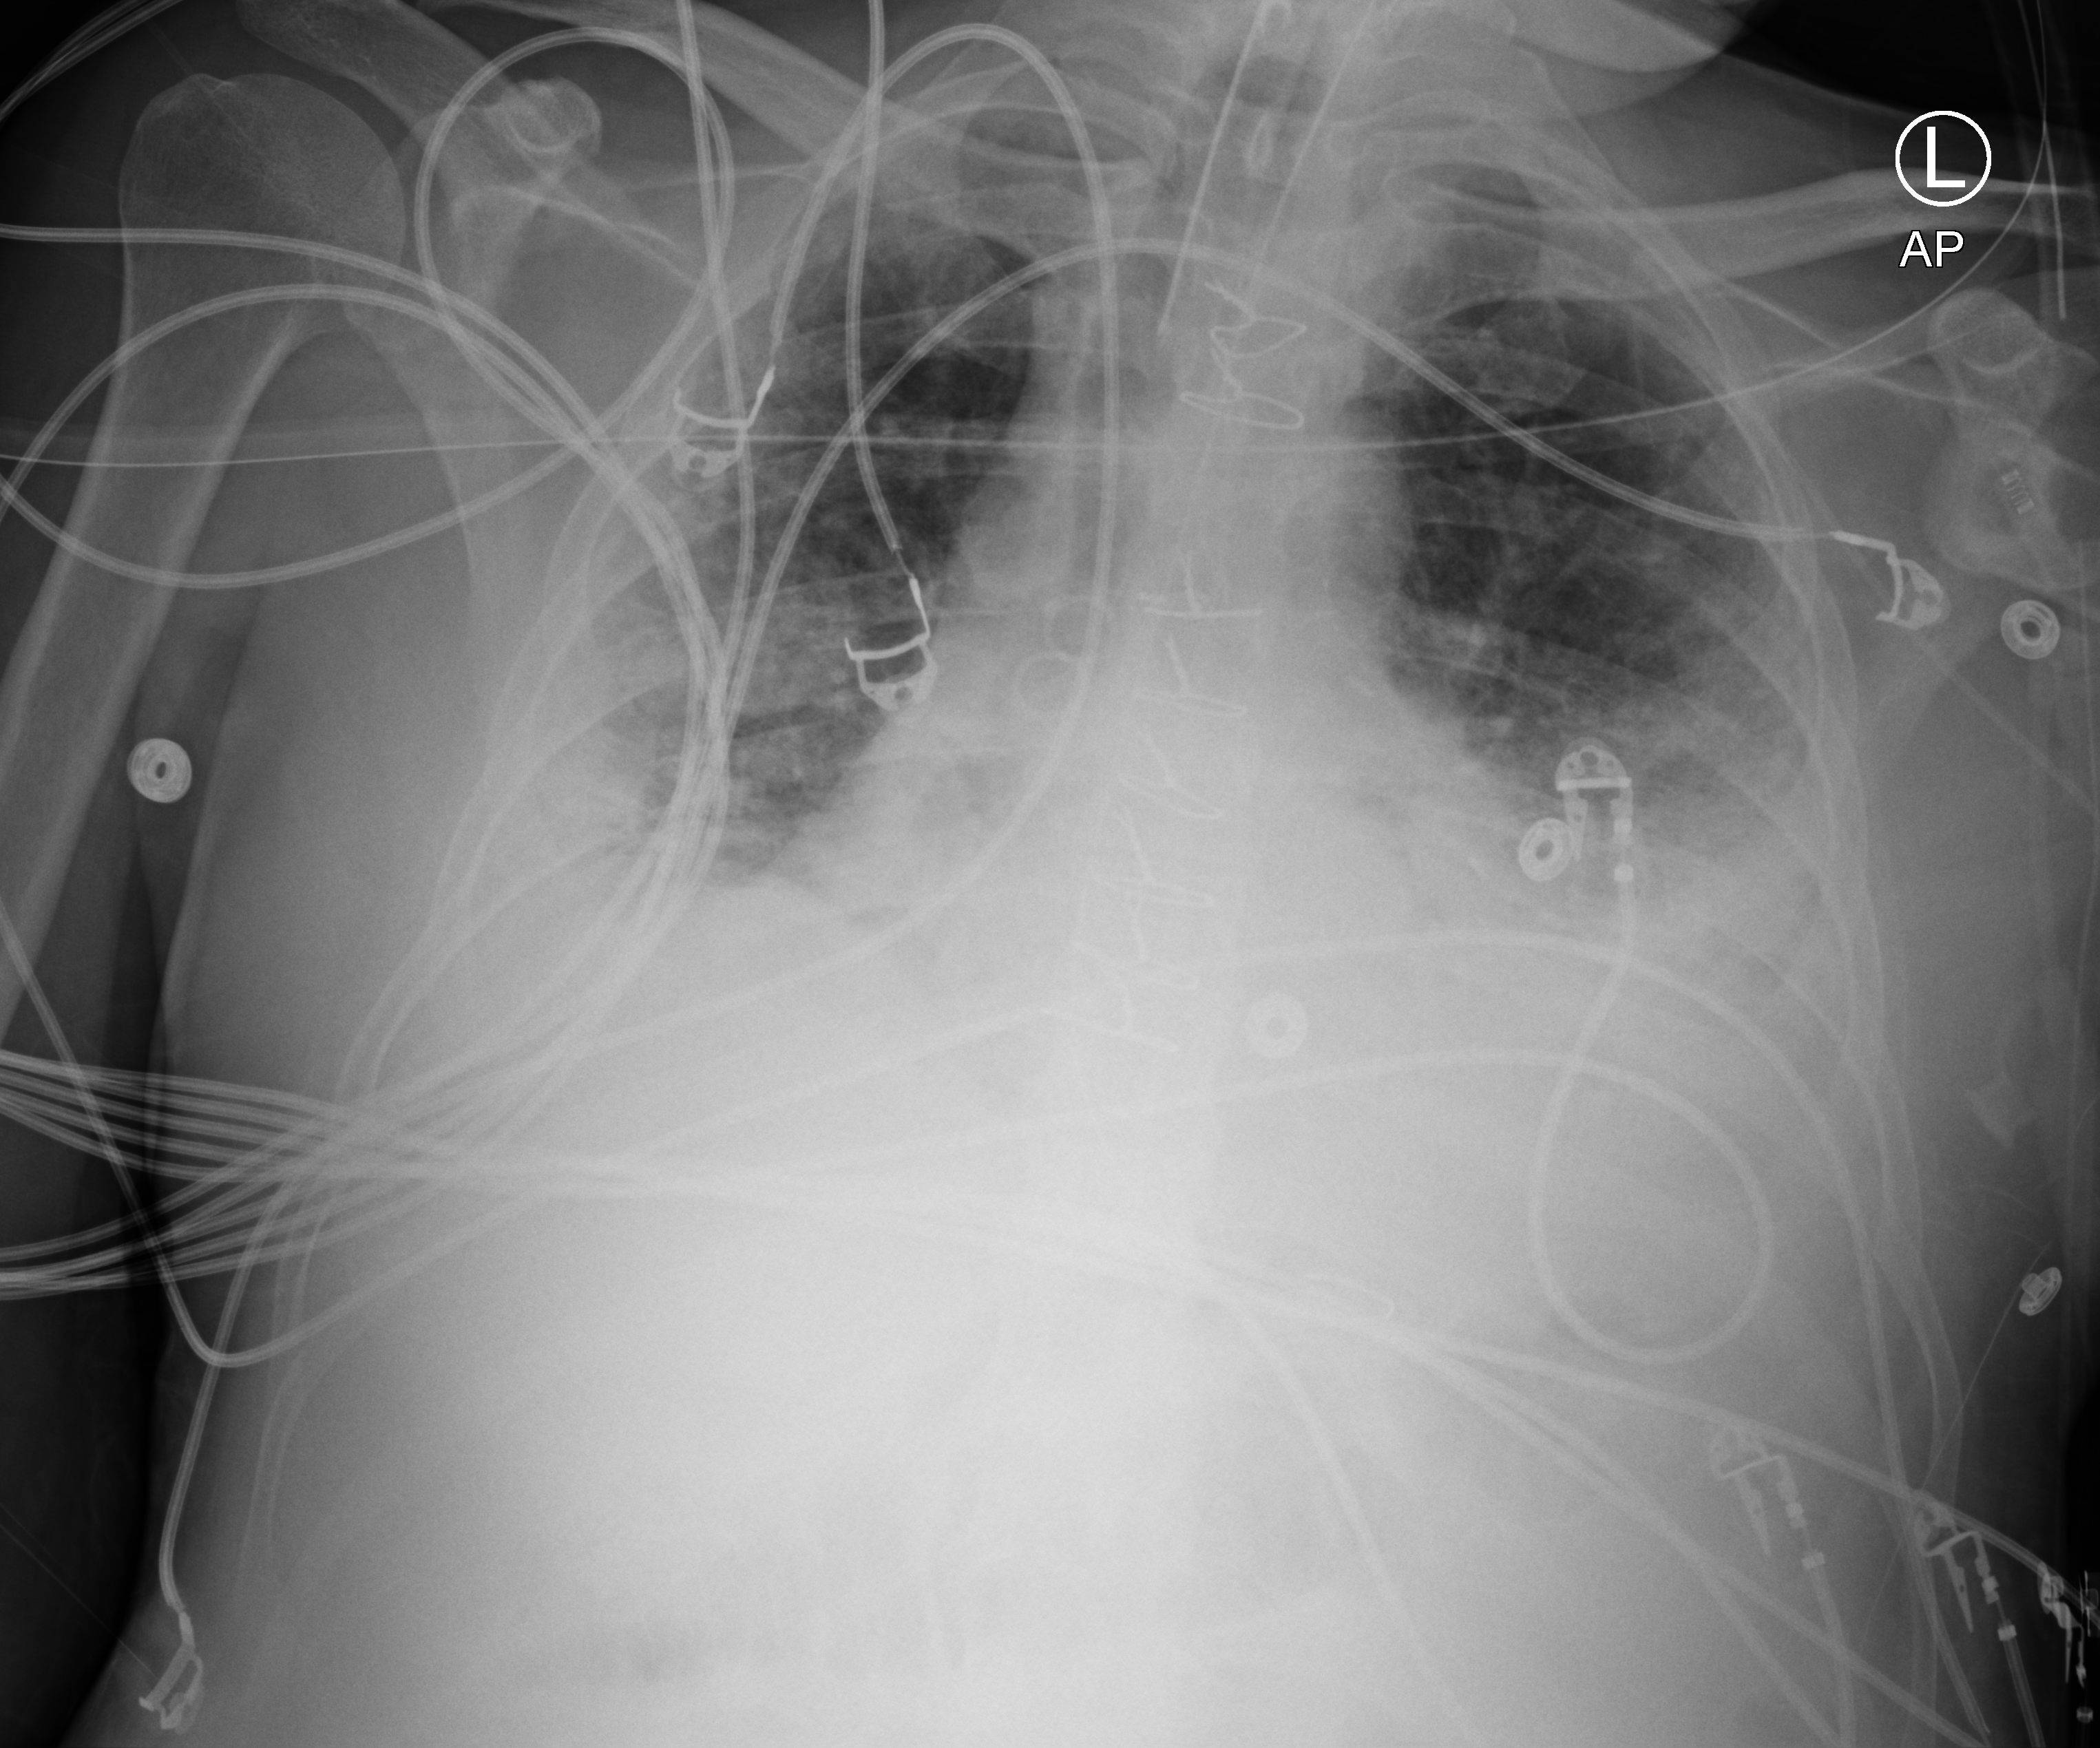
Bedside chest radiograph (computed radiography); anteroposterior (AP) projection. Patient hospitalised with COVID-19; male, aged 18–59 years.
From the hospital-stay record, not from the radiograph (when in the stay this image was taken is not recorded): length of hospital stay: 63 days; mechanically ventilated during this hospital stay: yes.